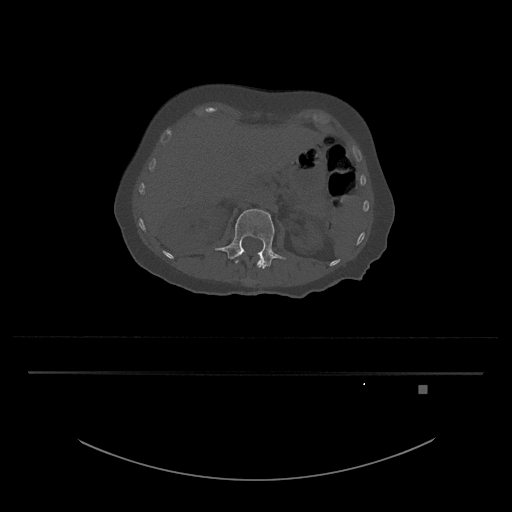
CT including the spine, one axial slice; slice 507 of 797 in the series (ordered by position); 120 kVp; bone window (W 1800 / L 400 HU); 512 × 512 image matrix. Patient: female, 57 years. From the clinical record (not read from this slice): primary cancer: cervical.
Annotated regions visible in this slice (semi-automatically segmented with operator editing):
- L1 vertebra: bounding box [x1, y1, x2, y2] px = [235, 250, 266, 268]